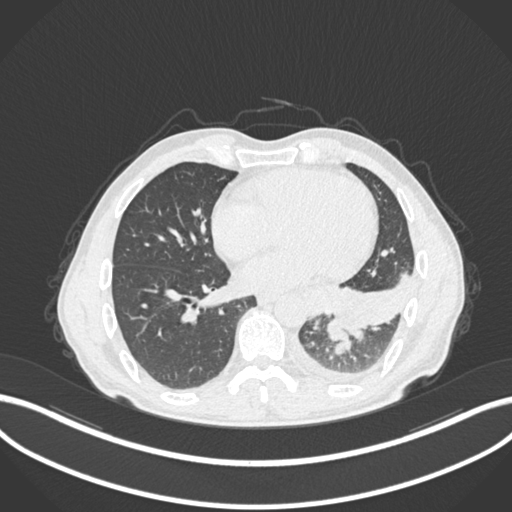
Chest CT, one axial slice. Reconstruction kernel B30f. Lung window (W 1500 / L -600 HU). 512 × 512 image matrix, field of view 400 × 400 mm. Male patient, age 47 years. From the clinical record (not read from this slice): clinical TNM (as recorded): T3 N1 M1c; histopathological grade: G3.
Annotated regions visible in this slice (rectangle marked by the reading radiologist):
- lung tumour (recorded histology: small cell carcinoma): bounding box <324,317,348,343> (left, top, right, bottom; pixels)